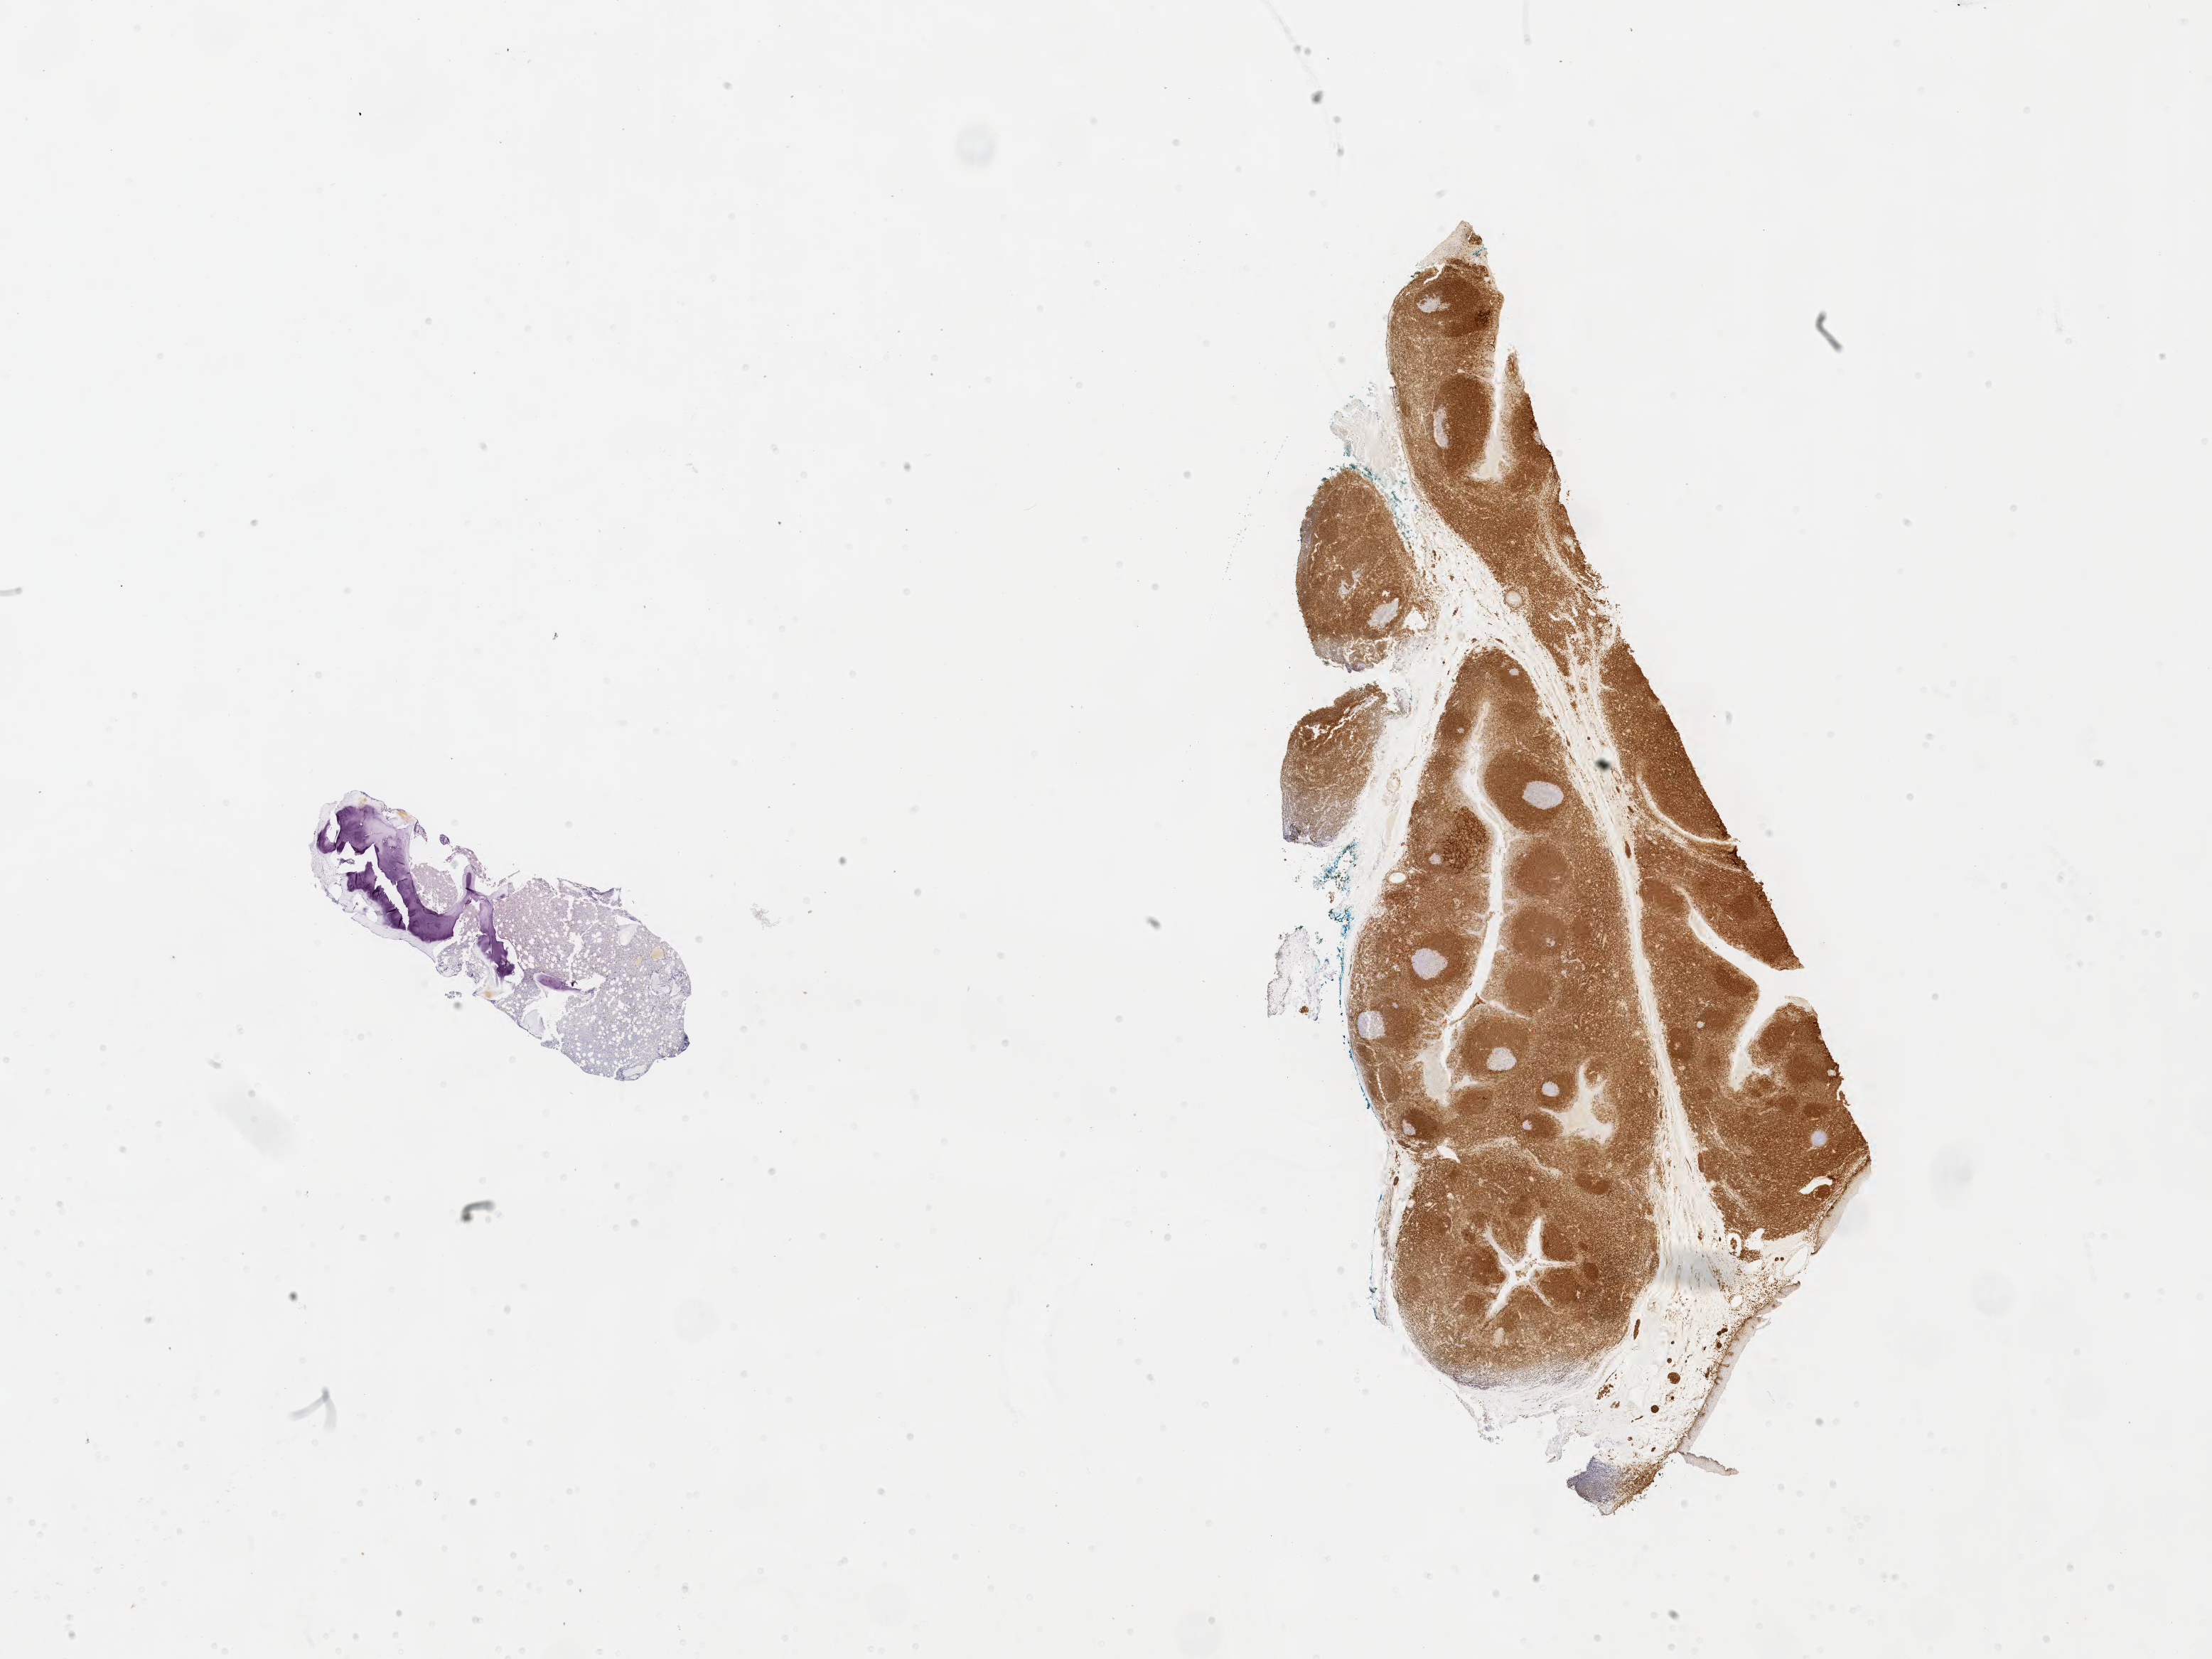
Immunohistochemistry (IHC) whole-slide image stained for BCL2, whole scanned area (about 25.1 x 18.9 mm) shown as a low-resolution overview. Specimen: tumor tissue. Anatomic site: bone marrow. Patient male; age 15 years.
• diagnosis: Burkitt lymphoma, NOS